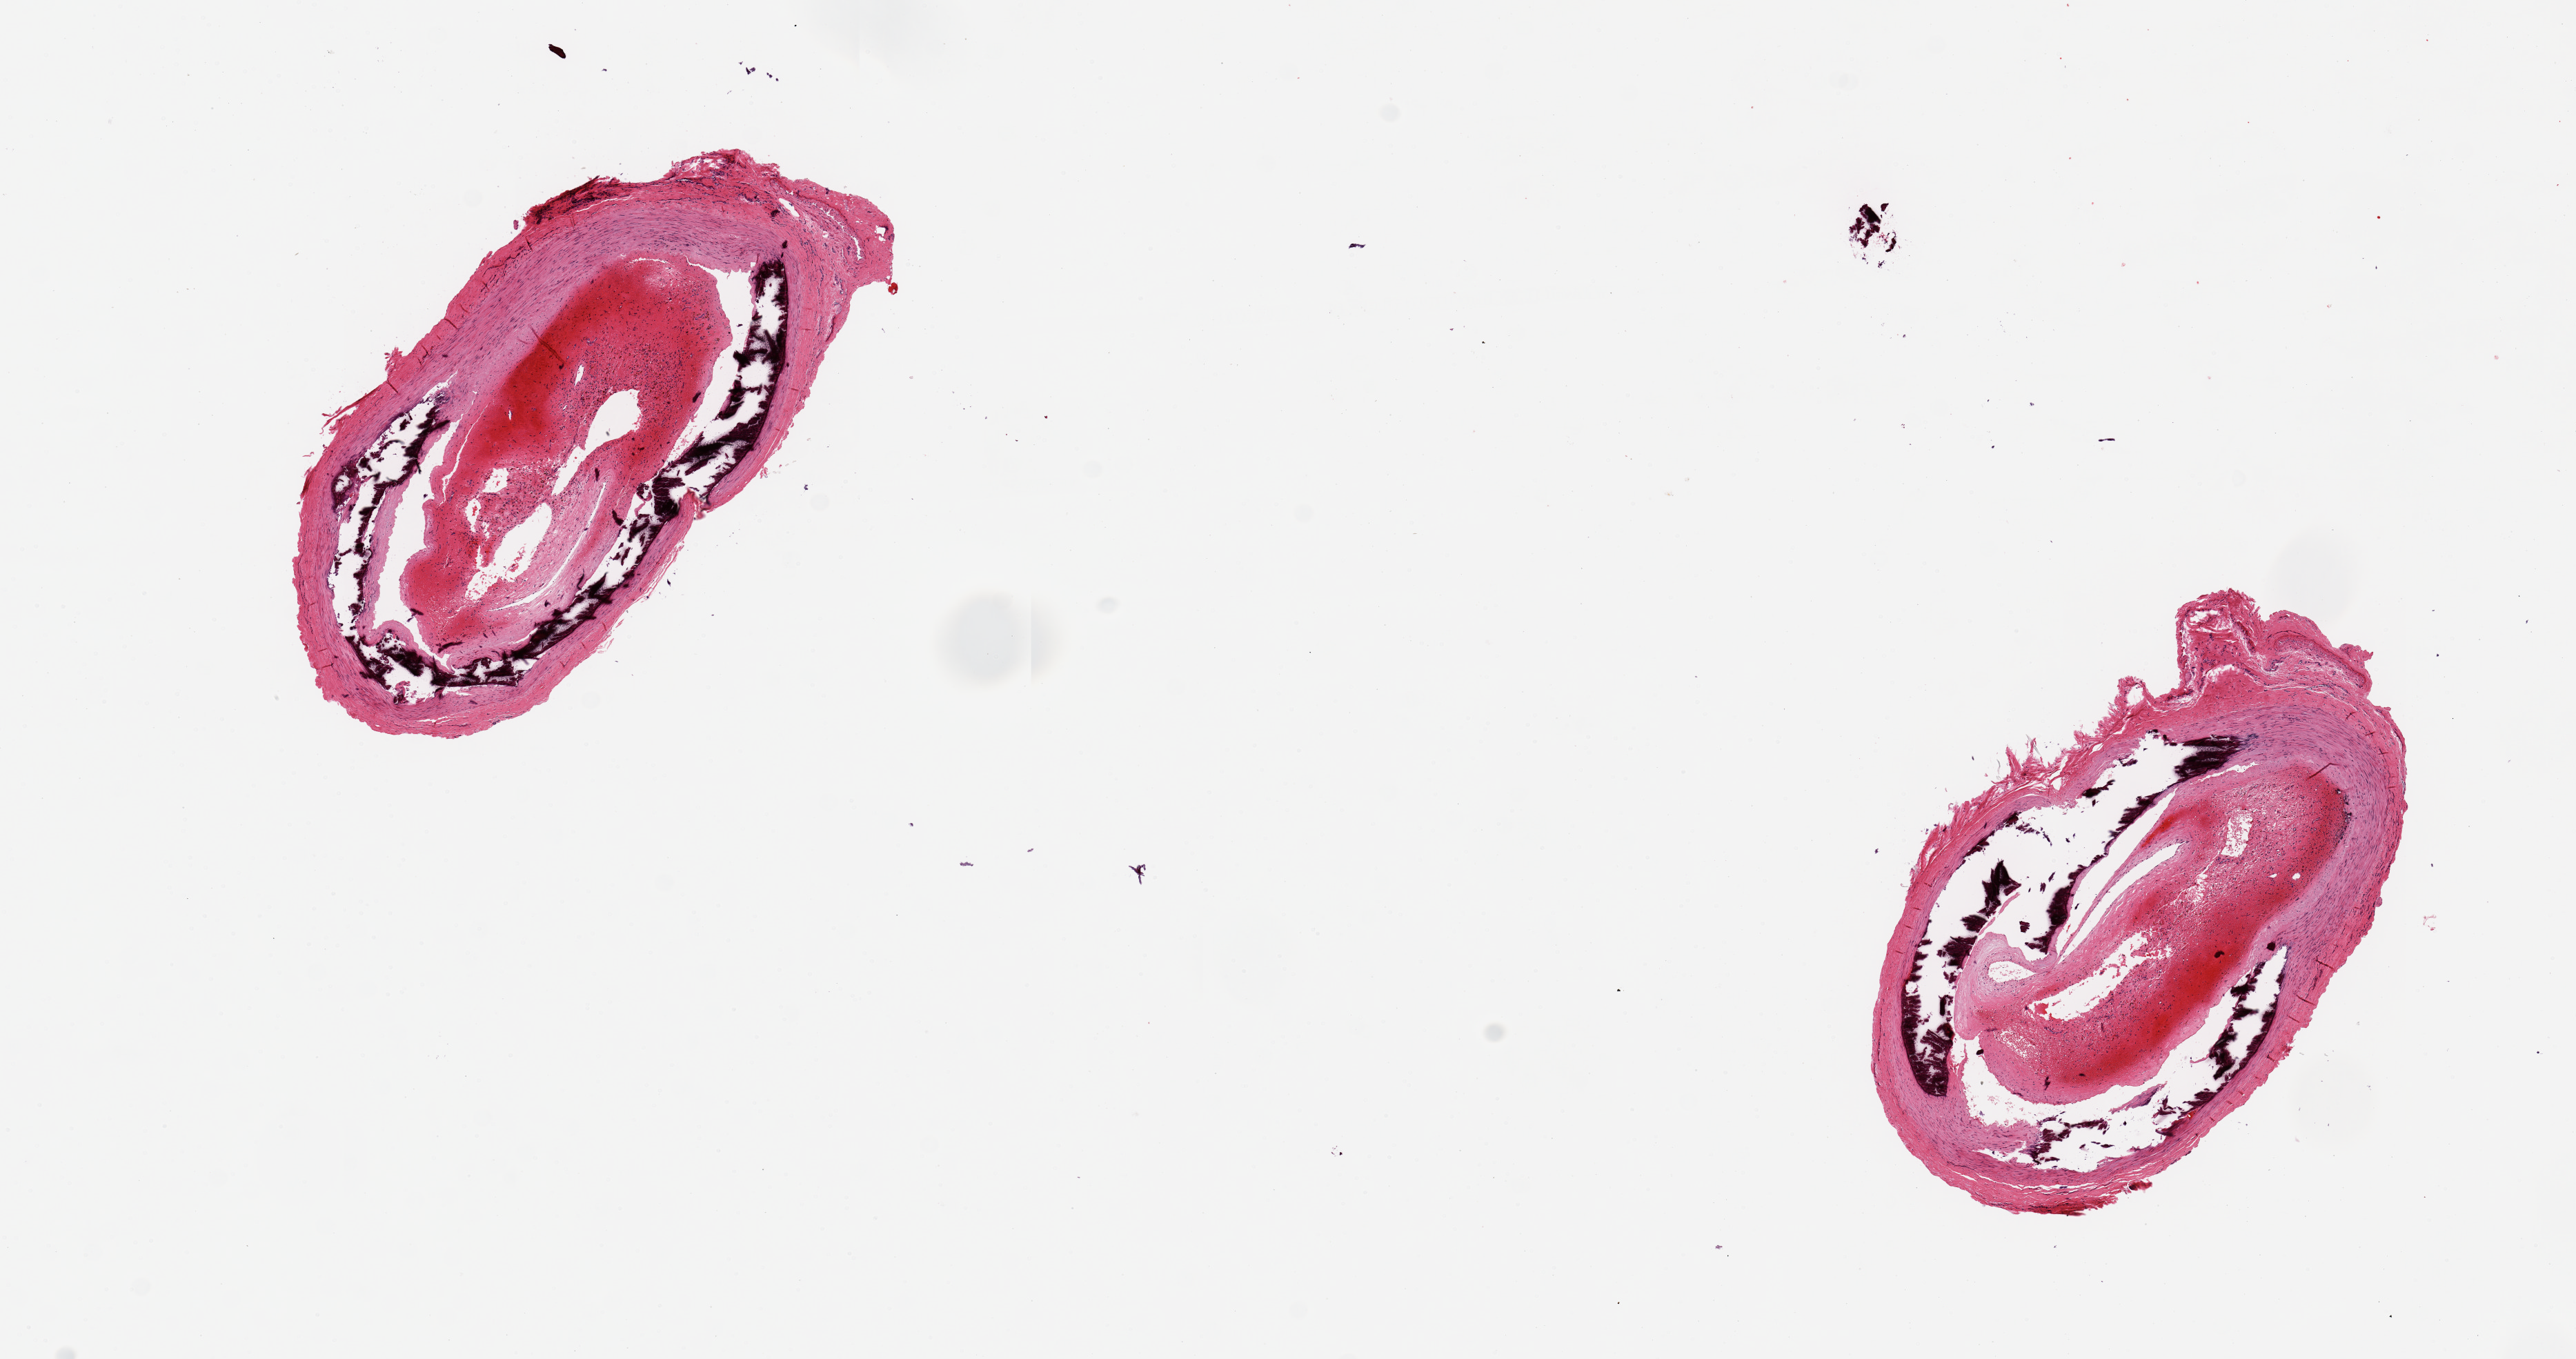
Digitized haematoxylin and eosin-stained section, low-resolution overview of the scanned area, about 14.8 x 7.8 mm. PAXgene-fixed paraffin-embedded (PFPE) section. Sampled site (target tissue): tibial artery. Donor tissue sample.
Review note (as recorded): 2 pieces 4x2 mm; severe Monckeberg sclerosis (medial calcification) and mural hemorrhage with greatly narrowed lumen.